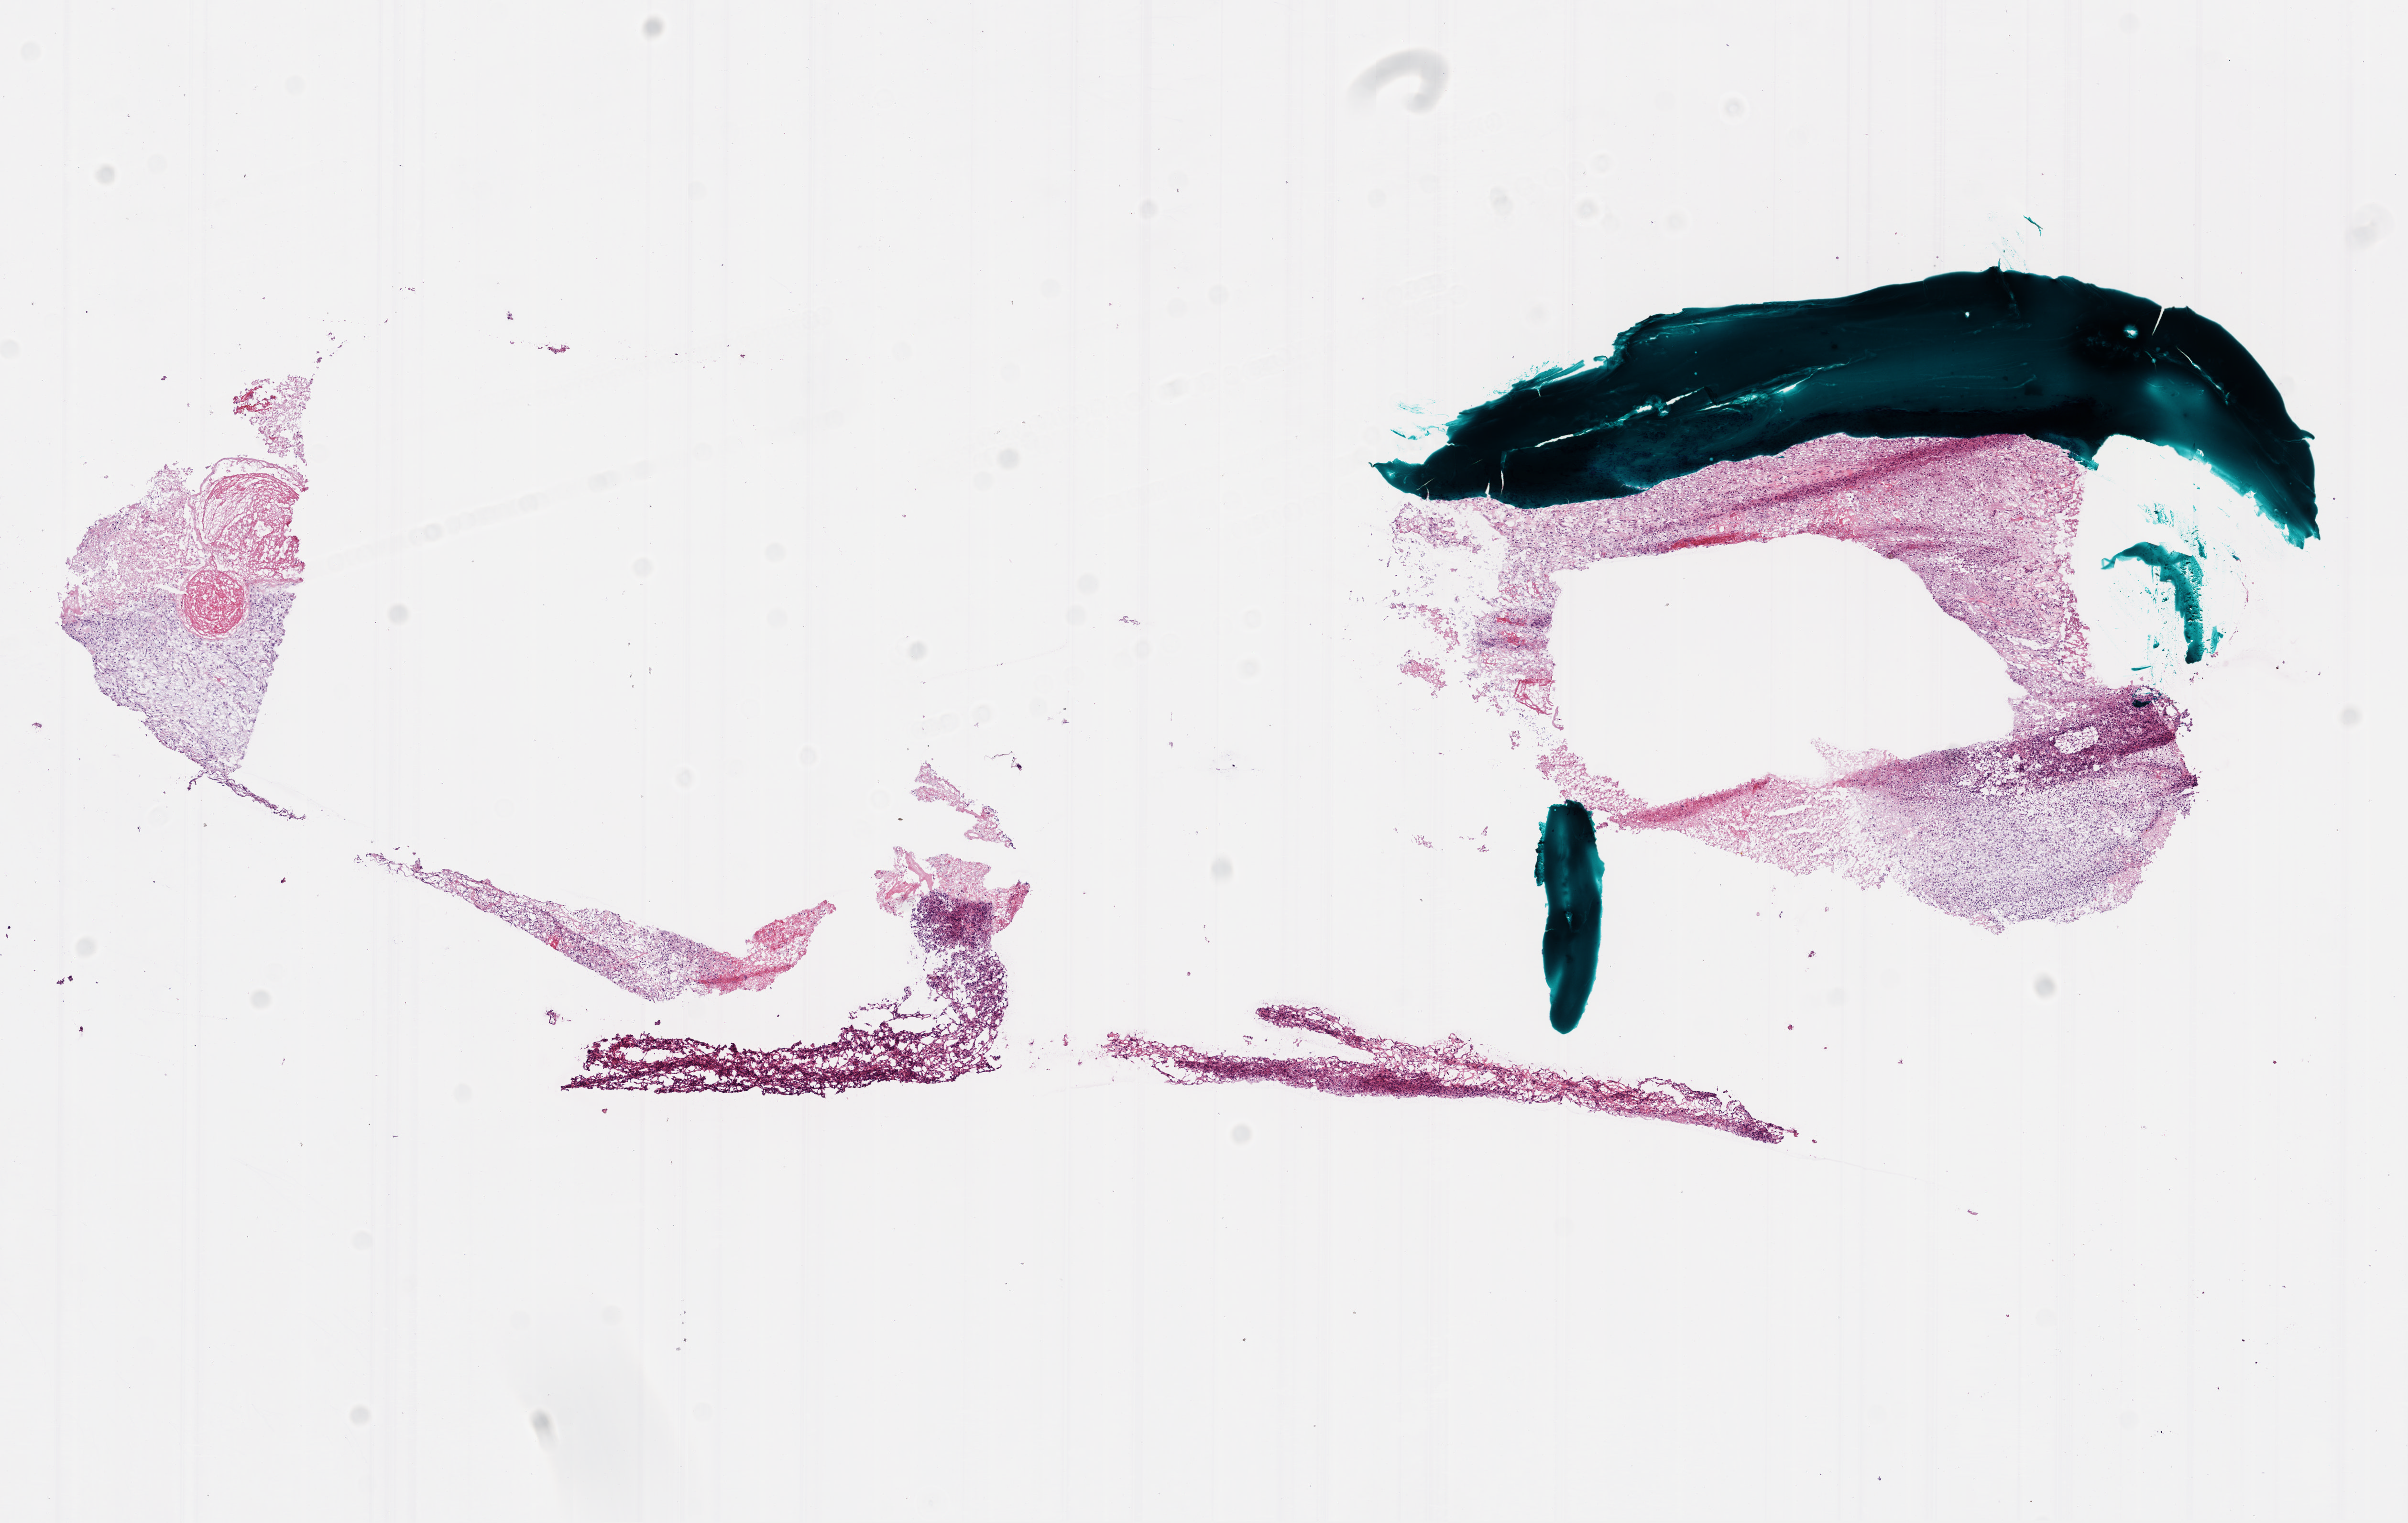
Hematoxylin and eosin (H&E) stained whole-slide image, whole scanned area (about 10.2 x 6.4 mm) shown as a low-resolution overview; frozen section; sample: primary tumour, brain. Patient: male, age at initial diagnosis 74 years. Slide review estimates, as recorded: tumour cells 75%, tumour nuclei 100%, normal cells 0%, stromal cells 0%, necrosis 25%.
- diagnosis: Glioblastoma